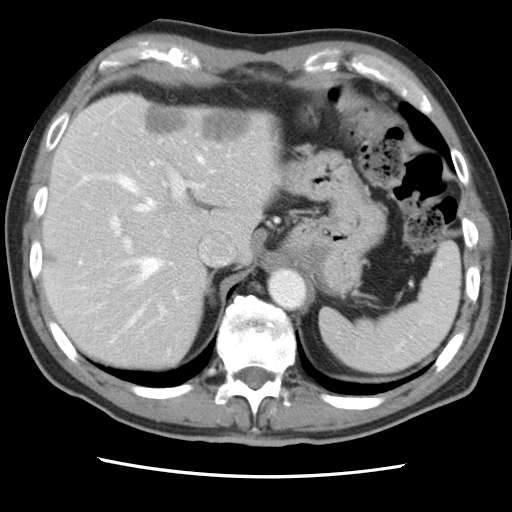
Contrast-enhanced abdominal CT, one axial slice; position 62 of 83 along the scan axis; 120 kVp; intravenous contrast given; soft-tissue window (W 400 / L 40 HU); 5 mm slice thickness; 512 × 512 image matrix, field of view 321 × 321 mm. Male patient, age 69 years. From the clinical record (not read from this slice): diagnosis: colorectal cancer liver metastases, imaged before liver resection; multiple liver metastases: yes; largest metastasis: 3.5 cm.
Outlined on this slice (expert manual segmentation):
- hepatic veins: box from (x=78, y=109) to (x=213, y=325) px
- liver: (x=44, y=94)–(x=274, y=369)
- planned liver remnant (the part of the liver to remain after resection): (x=44, y=144)–(x=211, y=369)
- portal vein (with intrahepatic branches): (x=110, y=161)–(x=204, y=314)
- liver metastasis: (x=145, y=106)–(x=187, y=134)
- liver metastasis: (x=203, y=111)–(x=251, y=142)